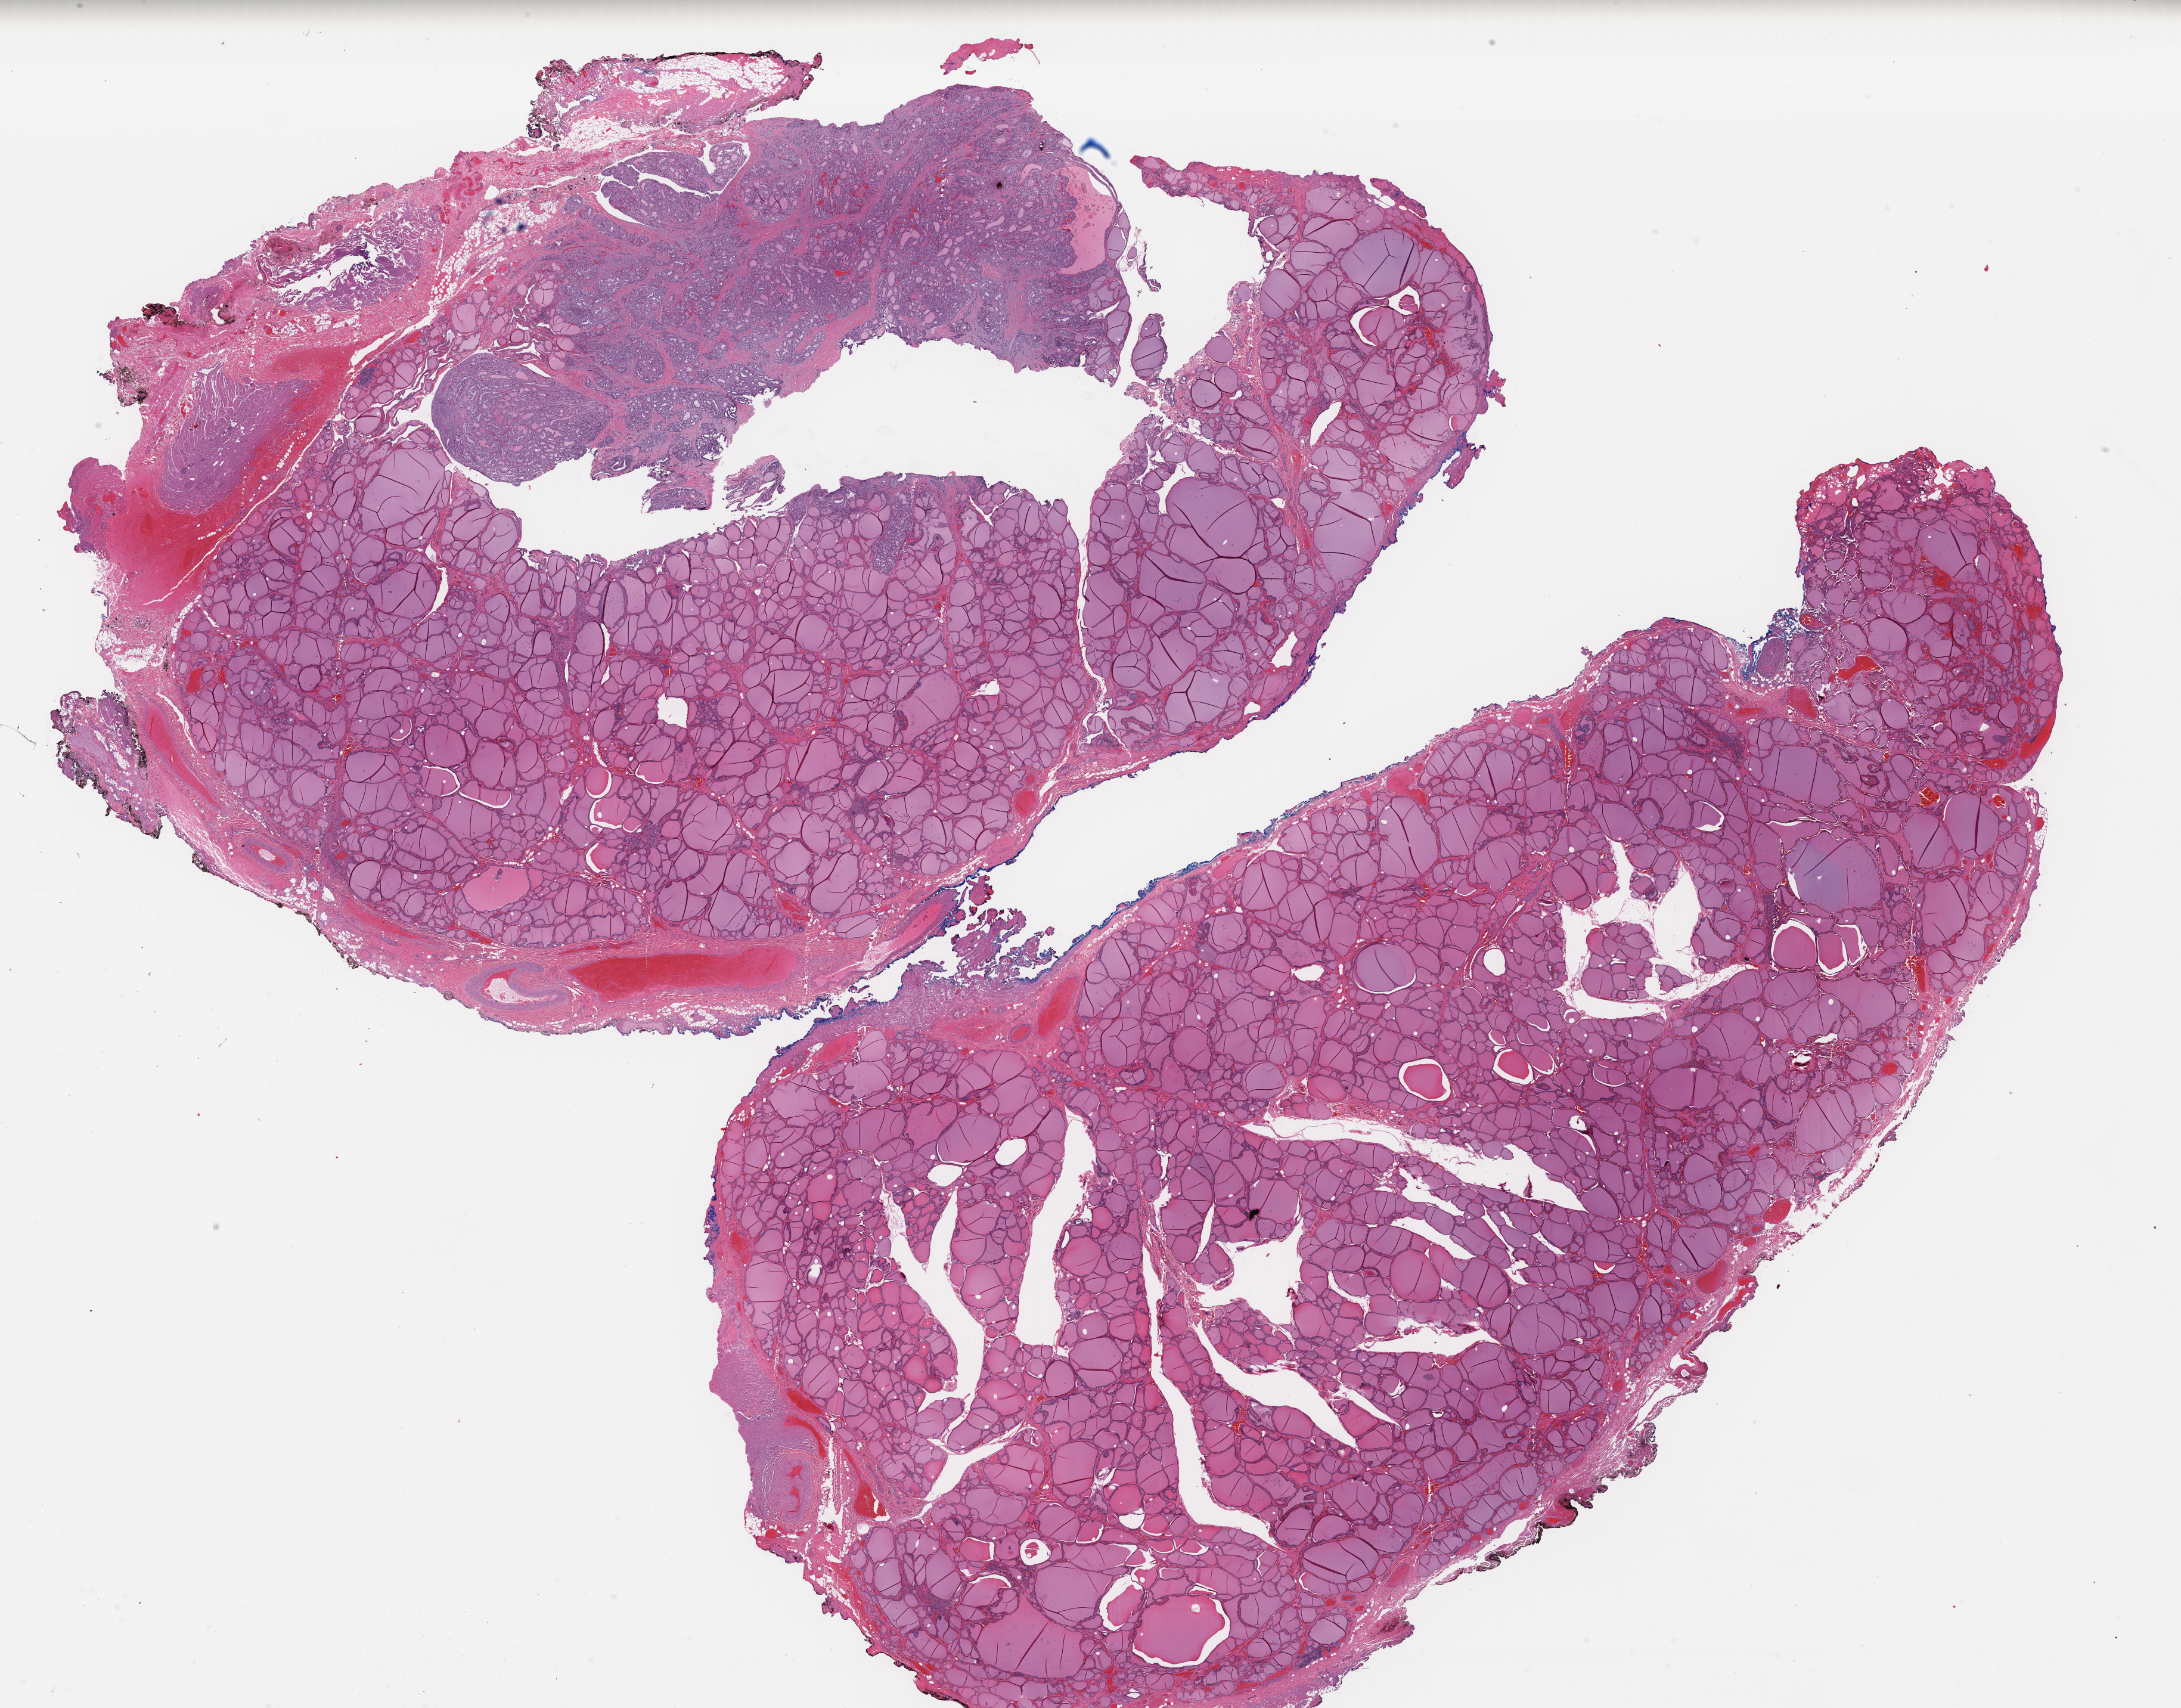
H&E whole-slide image, low-resolution overview of the scanned area, about 28.9 x 22.6 mm (slide scanned at 40x), formalin-fixed paraffin-embedded (FFPE) diagnostic section, sample: primary tumour, thyroid. Female patient; age at initial diagnosis 18 years.
- laterality: left
- TNM: T1 N0 M0
- AJCC pathologic stage: I (7th edition)
- histologic diagnosis: Papillary adenocarcinoma, NOS (thyroid gland)